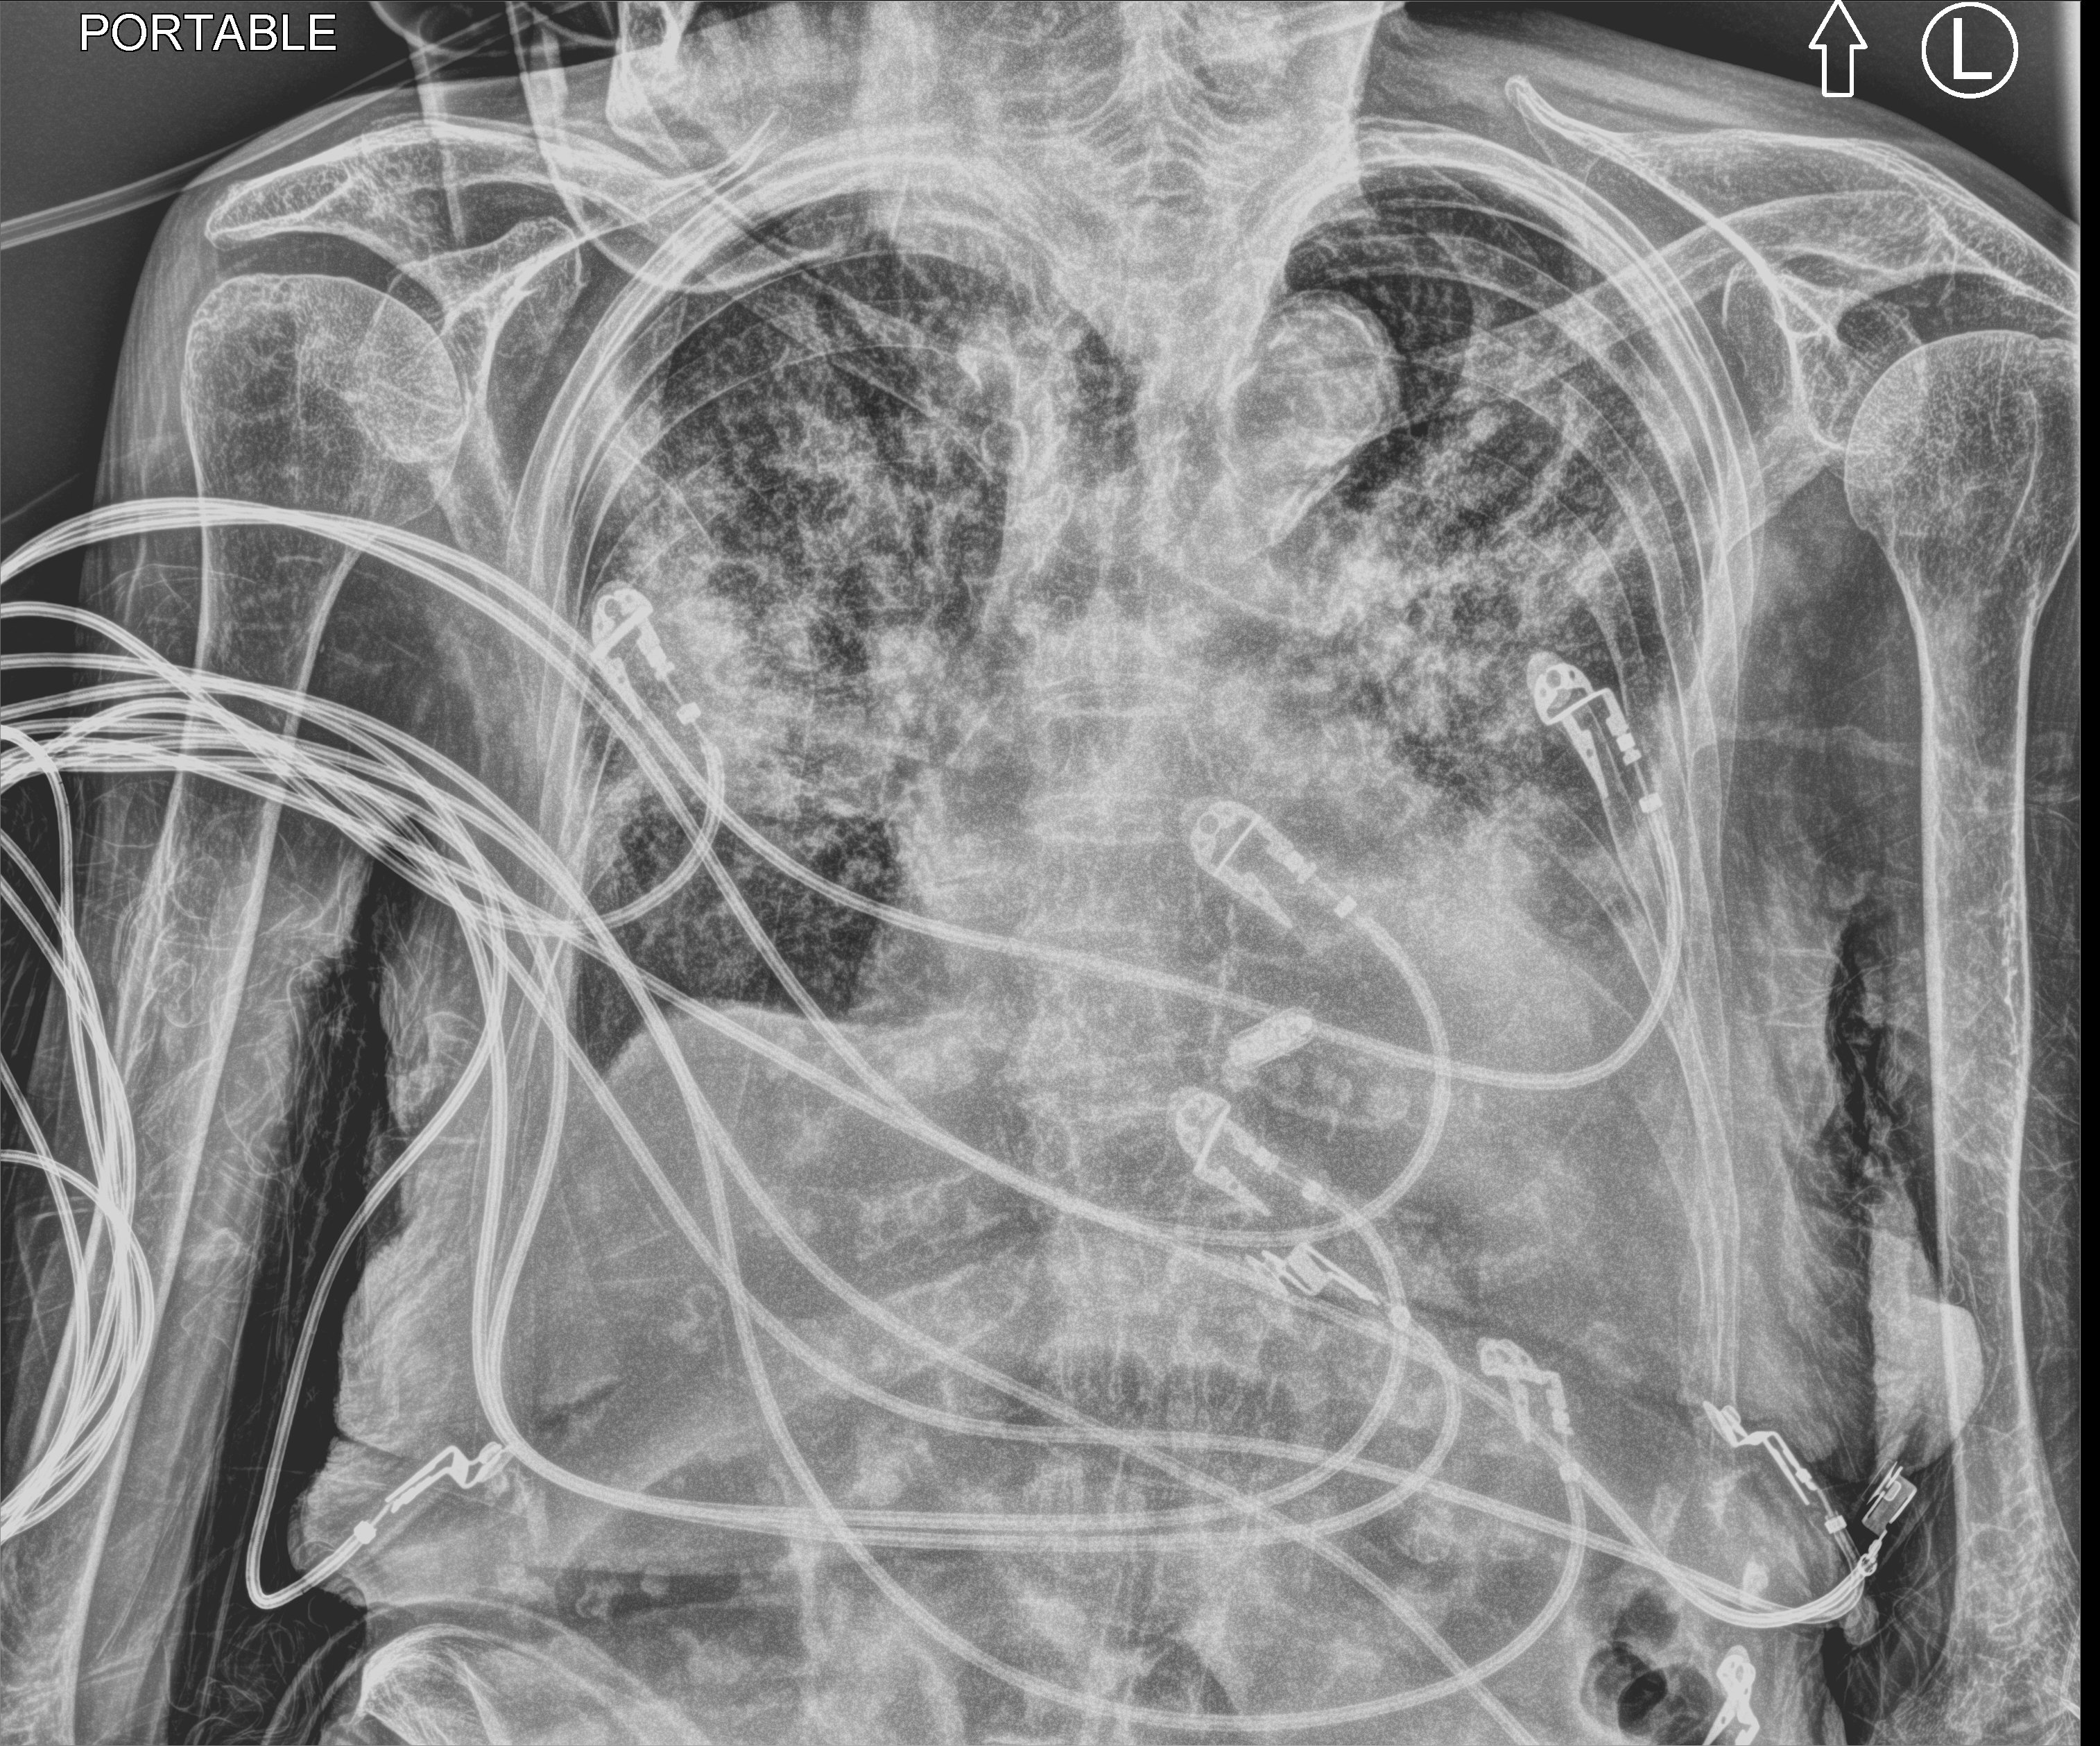
Bedside chest radiograph (computed radiography), anteroposterior (AP) projection. Patient hospitalised with COVID-19; female, aged 75–90 years.
Hospital-stay facts (about this admission, not read from this image; timing relative to this image not recorded):
- admitted to intensive care during this hospital stay: no